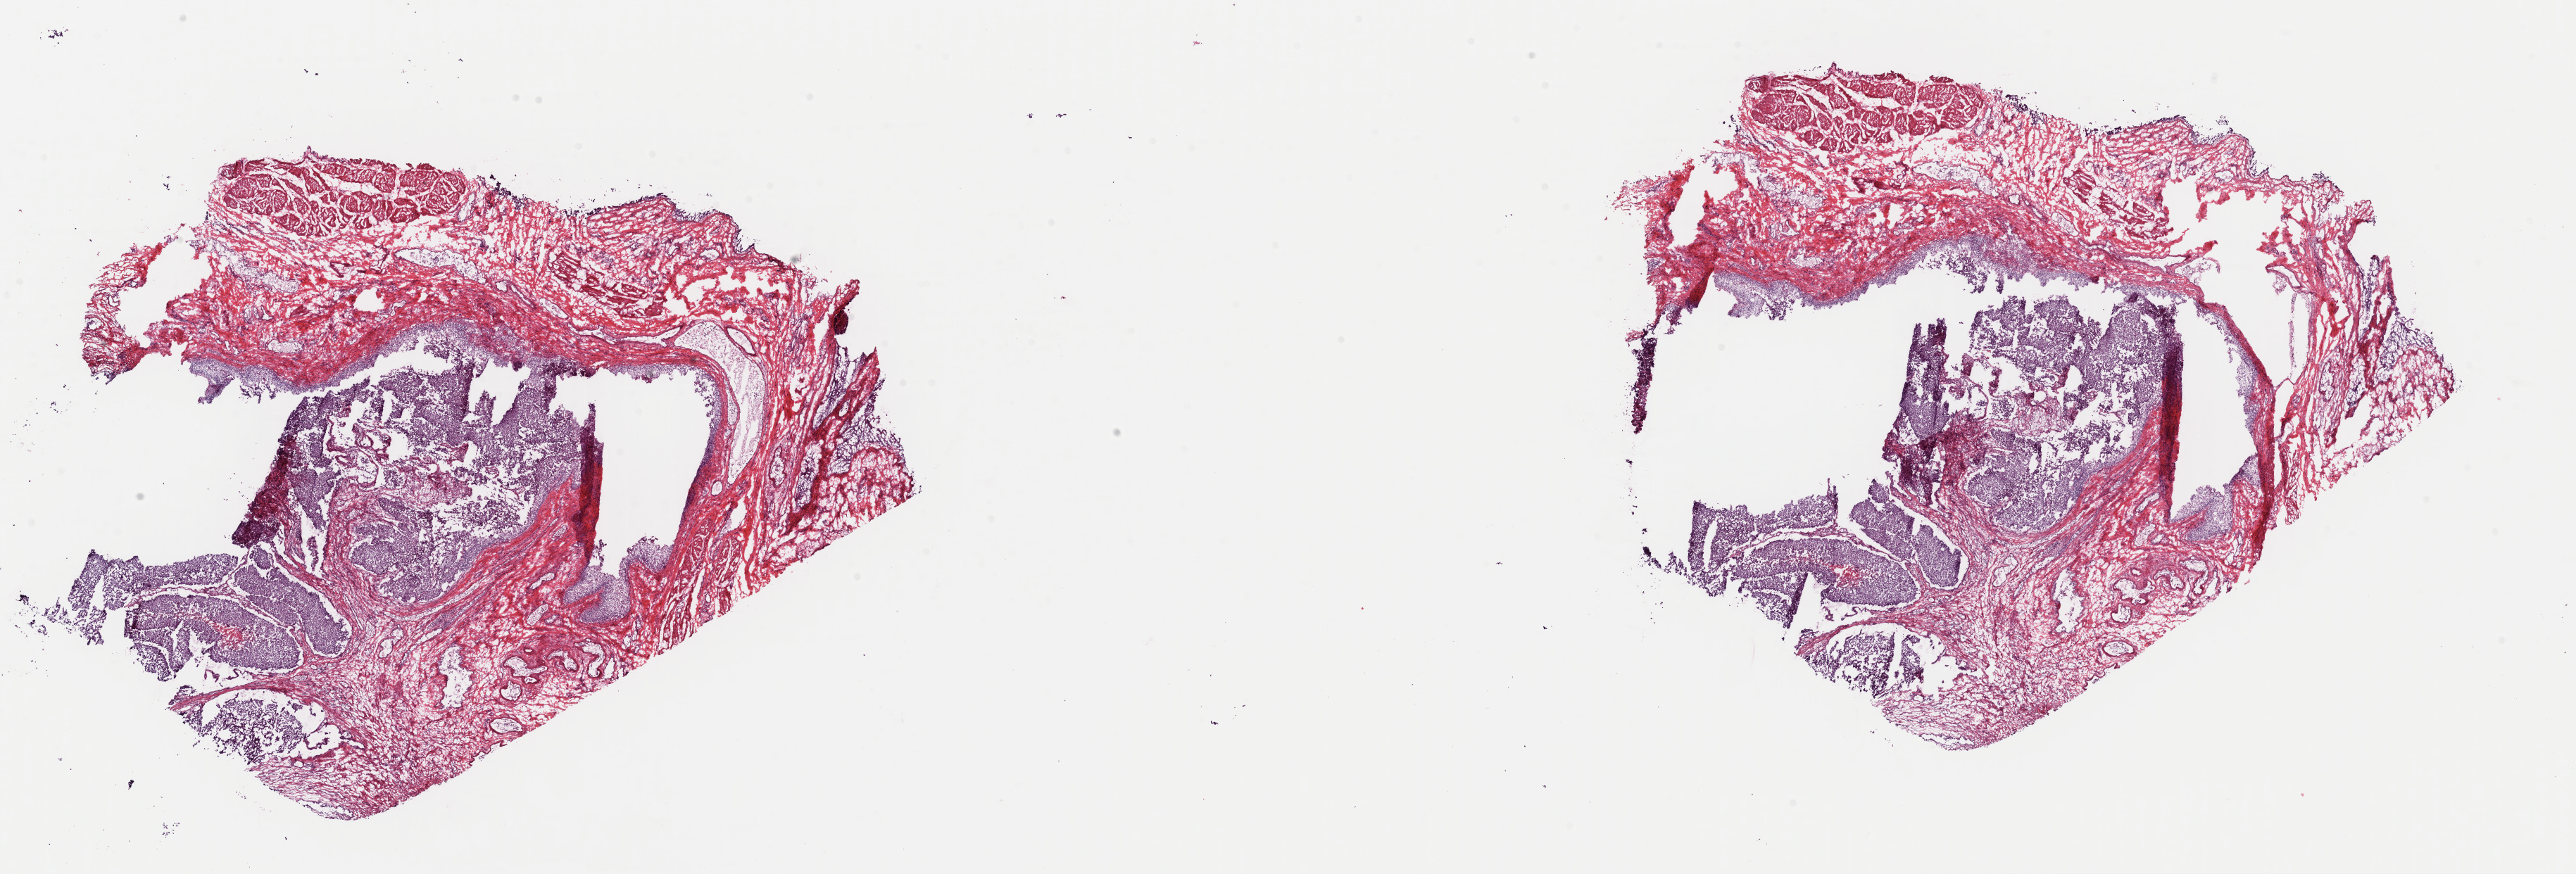
Whole-slide histology image, Hematoxylin and eosin (H&E) stained, a low-resolution overview of the entire scanned area, about 28.9 x 9.8 mm (from a 40x scan); frozen section; sample: primary tumour, bladder. Male, age 54 years at initial diagnosis. Slide review estimates, as recorded: tumour cells 37%, tumour nuclei 94%.
Pathologic diagnosis: Papillary transitional cell carcinoma (lateral wall of bladder).